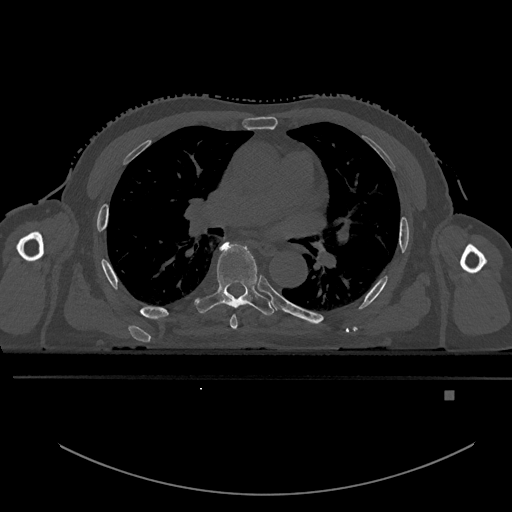
CT including the spine, one axial slice; position 318 of 969 along the scan axis; bone window (W 1800 / L 400 HU); 512 × 512 image matrix, field of view 456 × 456 mm. Male patient, age 82 years. From the clinical record (not read from this slice): primary cancer: prostate; vertebrae with lytic lesions (as recorded): T11, T9, T8, T2.
Structures marked on this image (semi-automatically segmented with operator editing):
- T5 vertebra: bounding box <230,314,238,329> (left, top, right, bottom; pixels)
- T6 vertebra: <195,241,276,316>